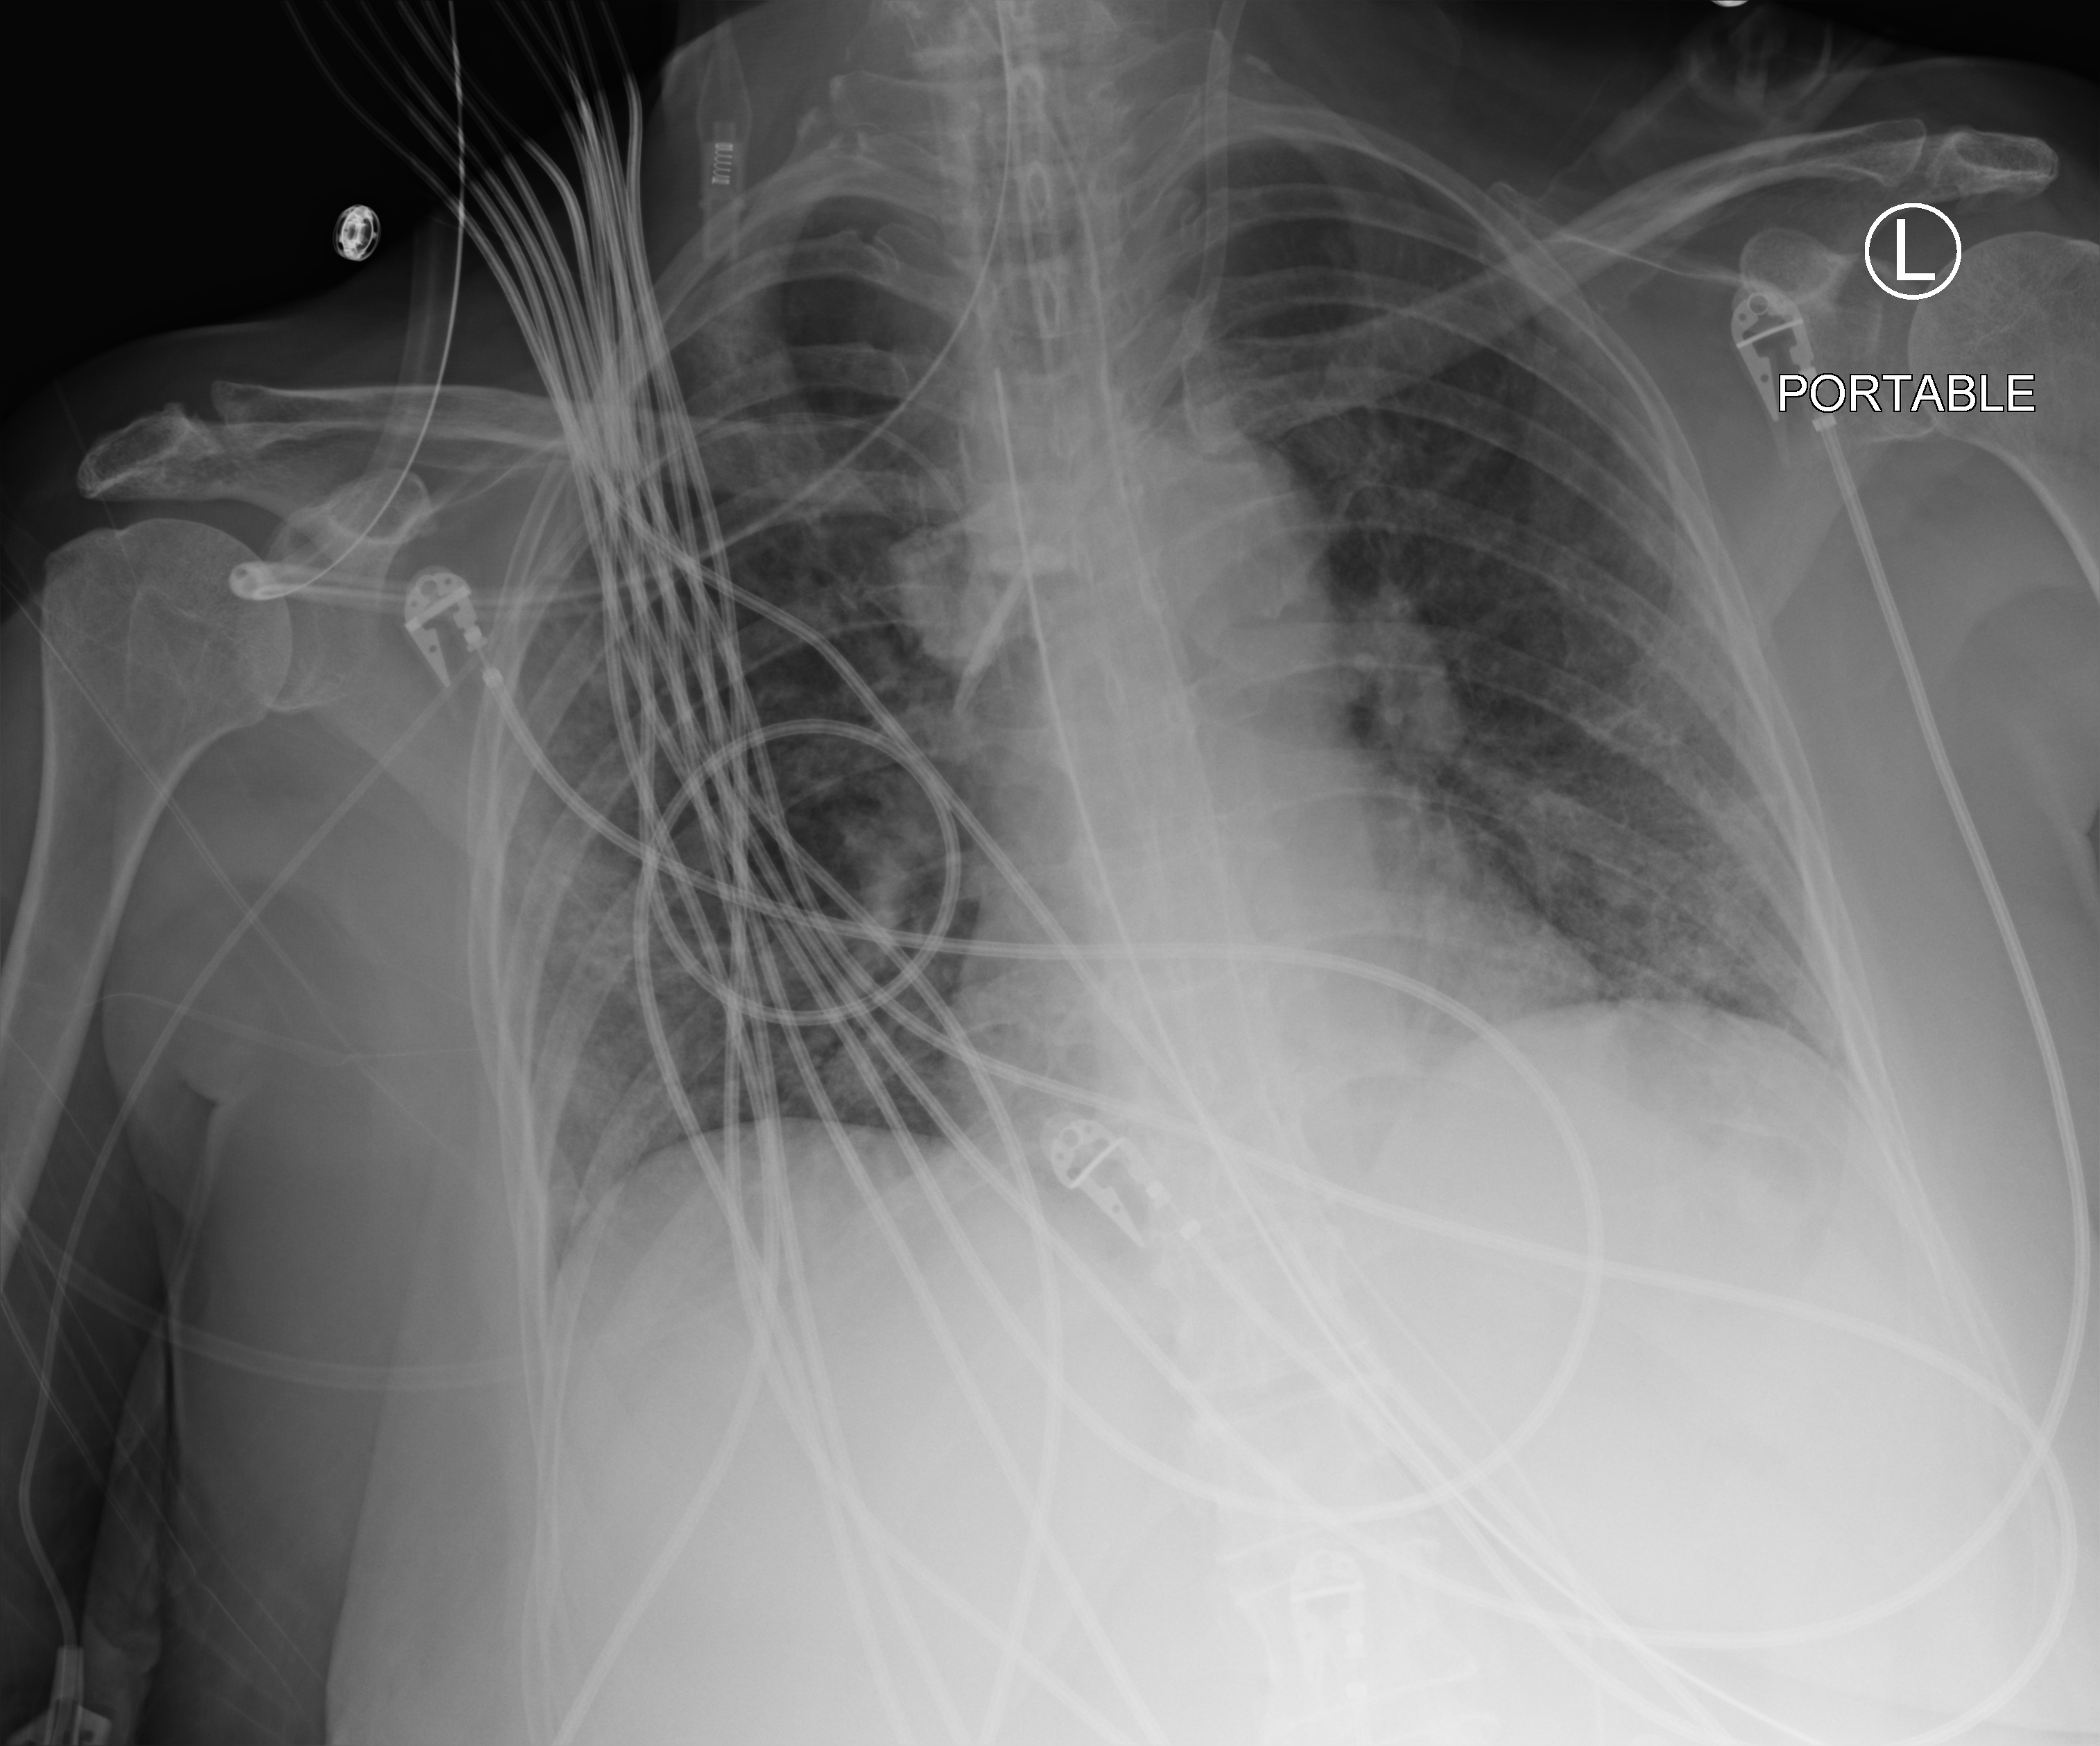
Portable chest radiograph; anteroposterior (AP) projection. Female patient hospitalised with COVID-19, age 60–74 years.
Admission-level facts for this patient (not findings on this image; timing relative to this image not recorded):
- length of hospital stay: 43 days